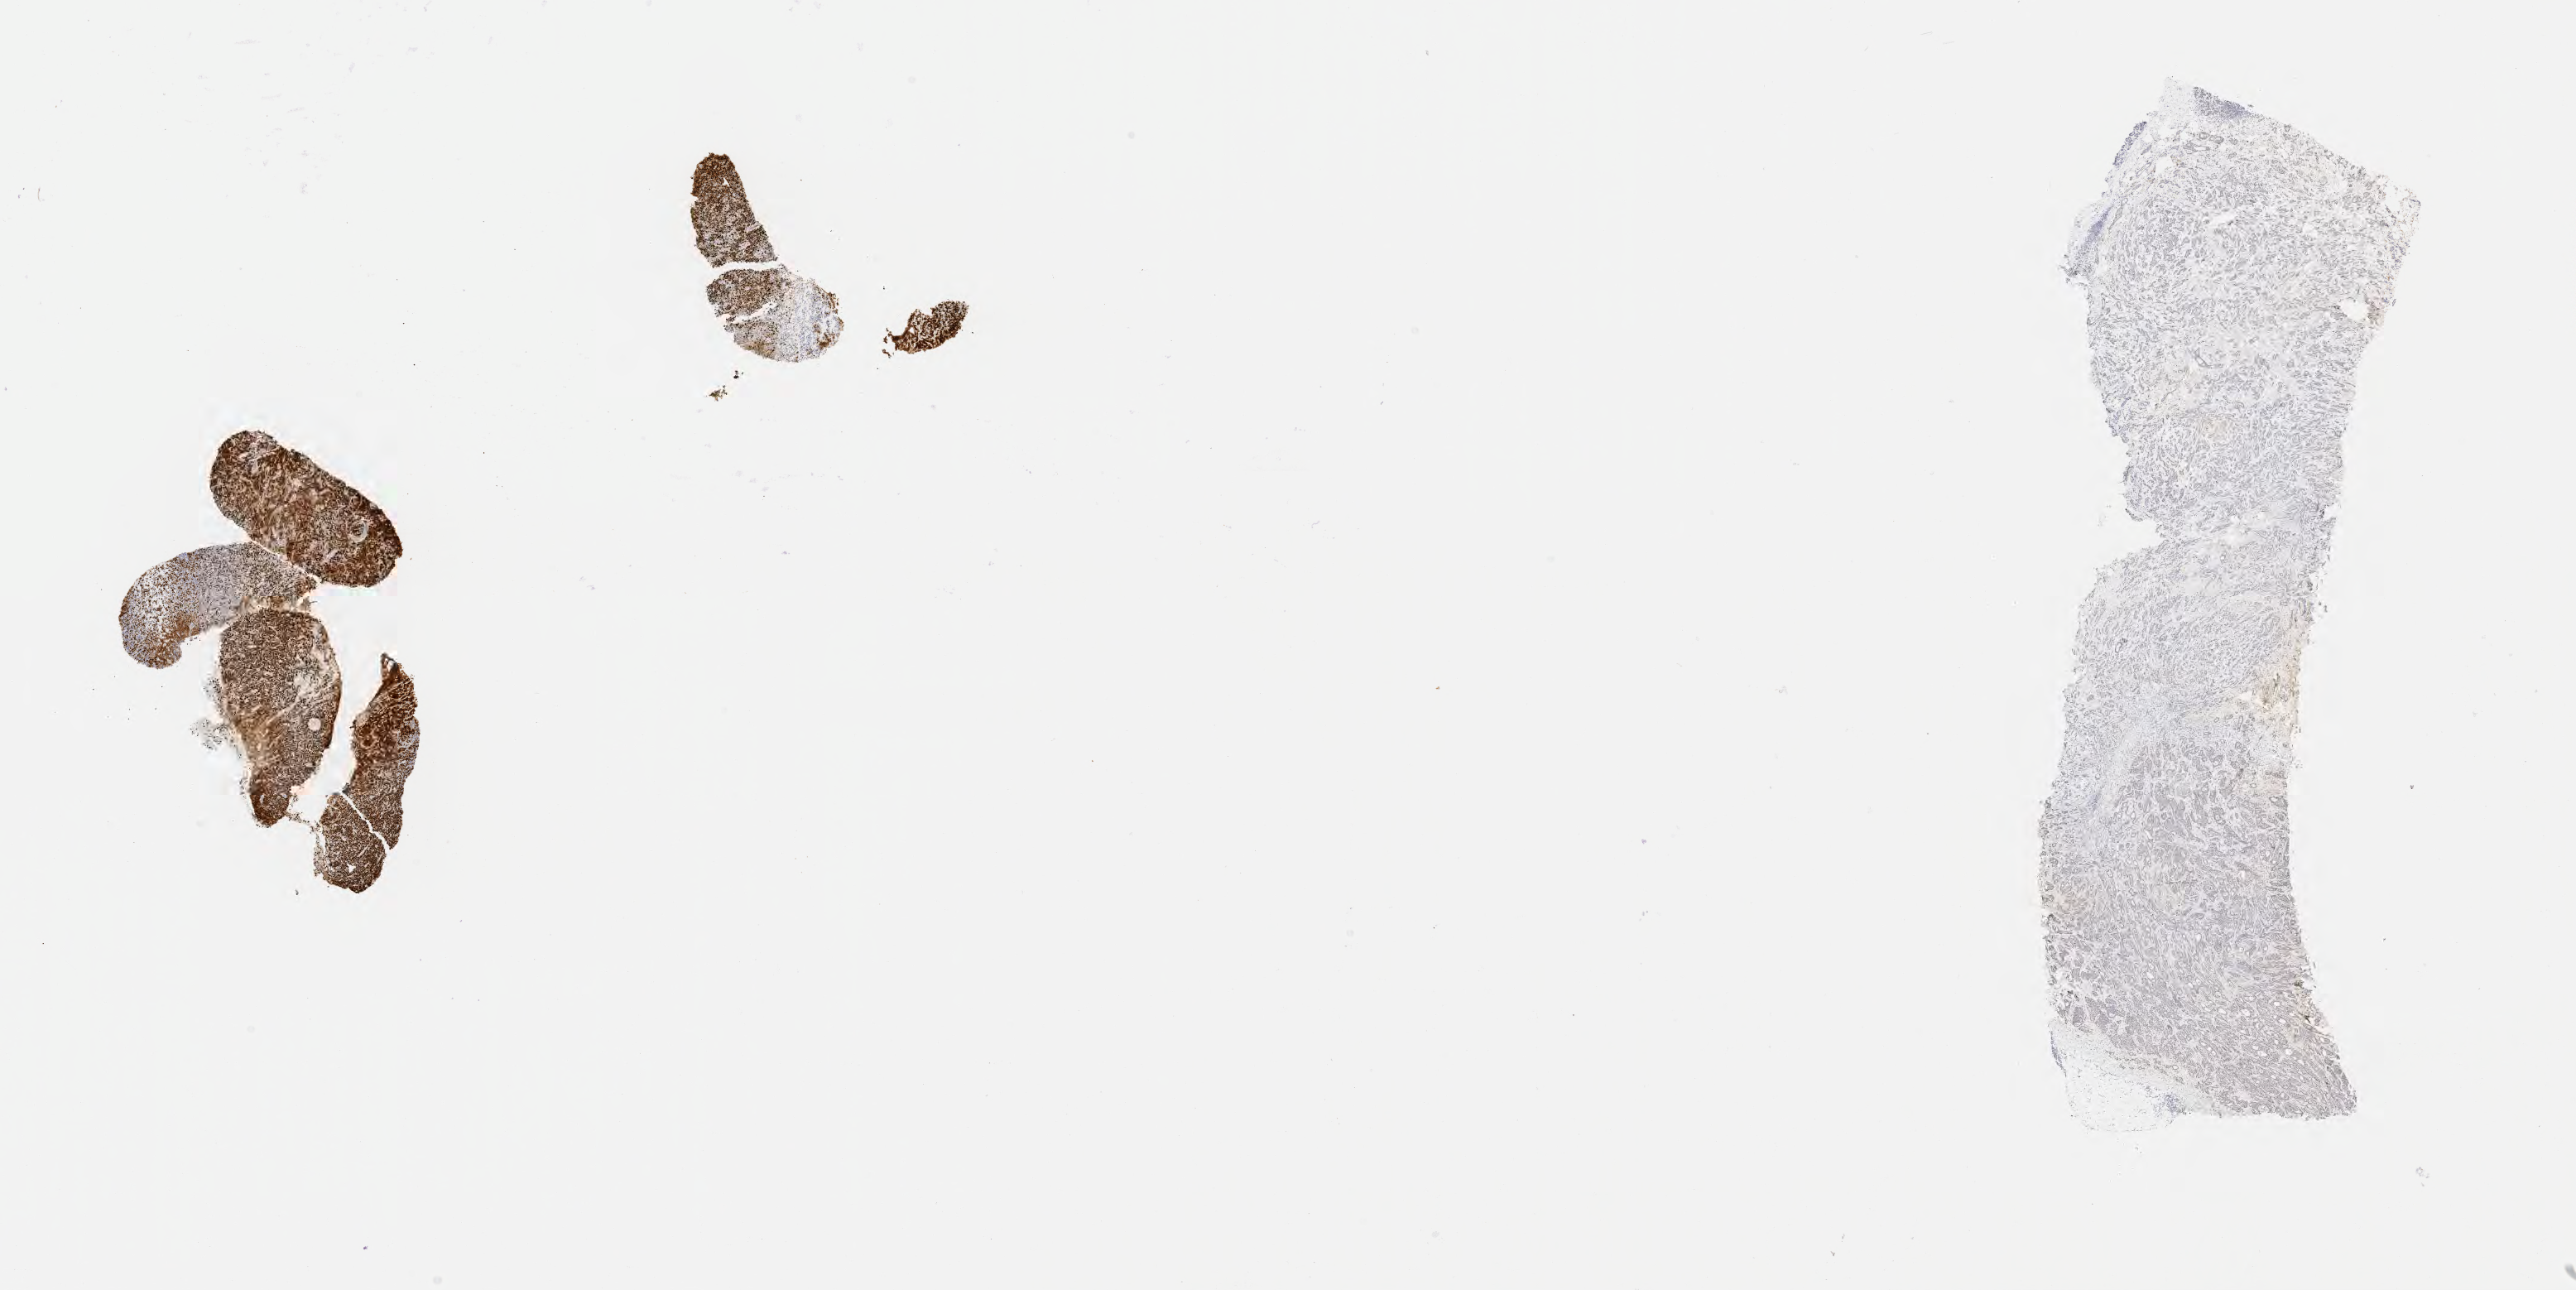
IHC for p53, whole-slide image, low-resolution overview of the scanned area, about 25.2 x 12.6 mm; tumor tissue; anatomic site: lymph node. Male patient, 54 years old.
Diagnosis: Diffuse large B-cell lymphoma, NOS.